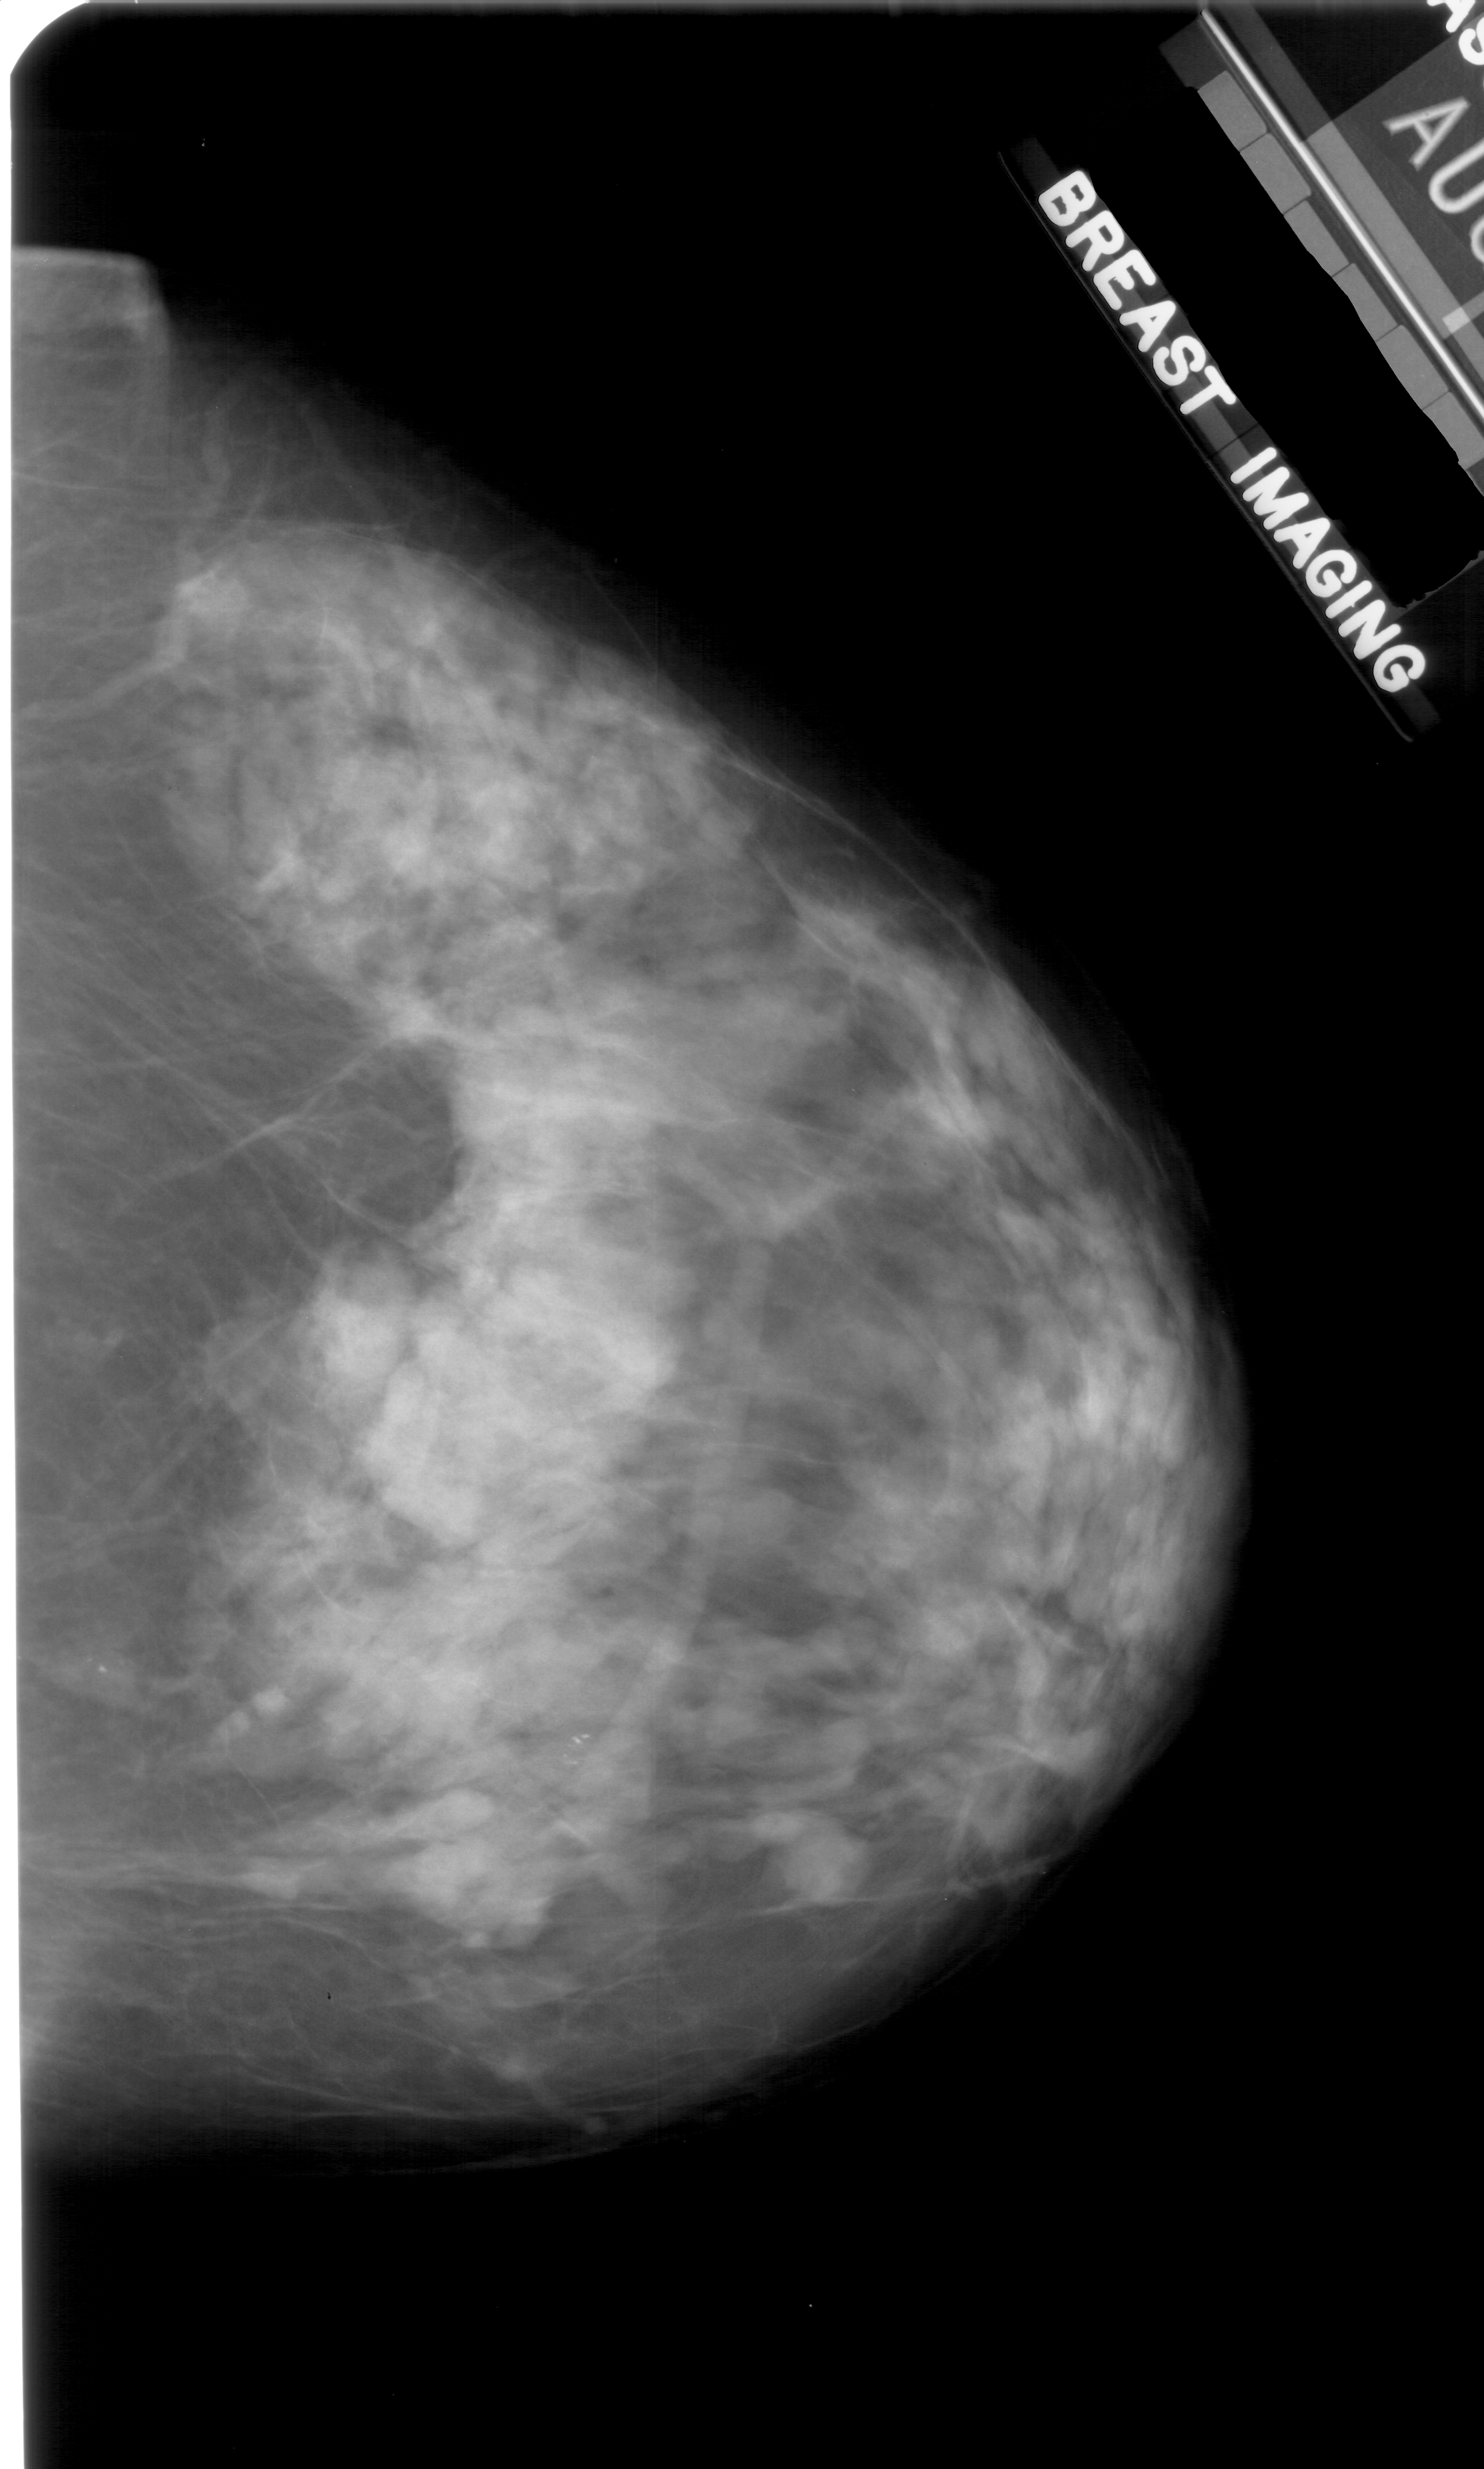
Scanned film-screen mammogram. Right breast. CC view. Breast composition: heterogeneously dense (BI-RADS density category 3 of 4). 1484 × 2469 image matrix.
Expert-marked regions of interest on this image (one box per marked abnormality):
- calcifications, morphology pleomorphic, distribution clustered; BI-RADS assessment category 4; pathology (as recorded): benign: bounding box [x1, y1, x2, y2] px = [560, 1716, 610, 1766]